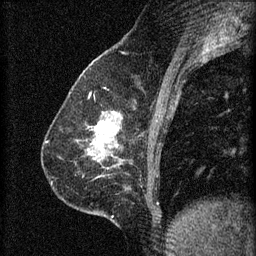
Breast MRI (dynamic contrast-enhanced), one sagittal slice; slice 25 of 60 in the series (ordered by position); 3 images stored at this slice position (order not interpretable as contrast timing); 1.5 T; TE 4.2 ms, TR 8.2 ms; 2 mm slice thickness; 256 × 256 image matrix, field of view 180 × 180 mm. Female patient, age 59 years.
Structures marked on this image (semi-automatic segmentation, software-assisted and operator-edited):
- analysis volume of interest (the breast-tissue region the enhancement analysis was run in; not a lesion): bounding box [x1, y1, x2, y2] px = [61, 104, 125, 161]
- tumour enhancement mask (voxels above the 70 % enhancement threshold inside the analysis volume of interest): [93, 122, 117, 145]